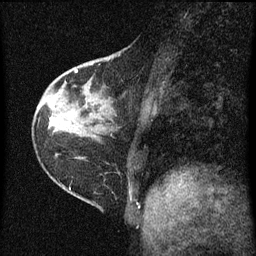
Breast MRI (dynamic contrast-enhanced), one sagittal slice; dynamic contrast-enhanced series, image 2 of 3 at this slice position (ordered by acquisition); 1.5 T; TE 4.2 ms, TR 8 ms; 2 mm slice thickness; 256 × 256 image matrix. Patient: female, 38 years.
Outlined on this slice (semi-automatically segmented with operator editing):
- analysis volume of interest (the breast-tissue region the enhancement analysis was run in; not a lesion): bounding box <67,50,125,131> (left, top, right, bottom; pixels)
- tumour enhancement mask (voxels above the 70 % enhancement threshold inside the analysis volume of interest): <75,60,109,73>